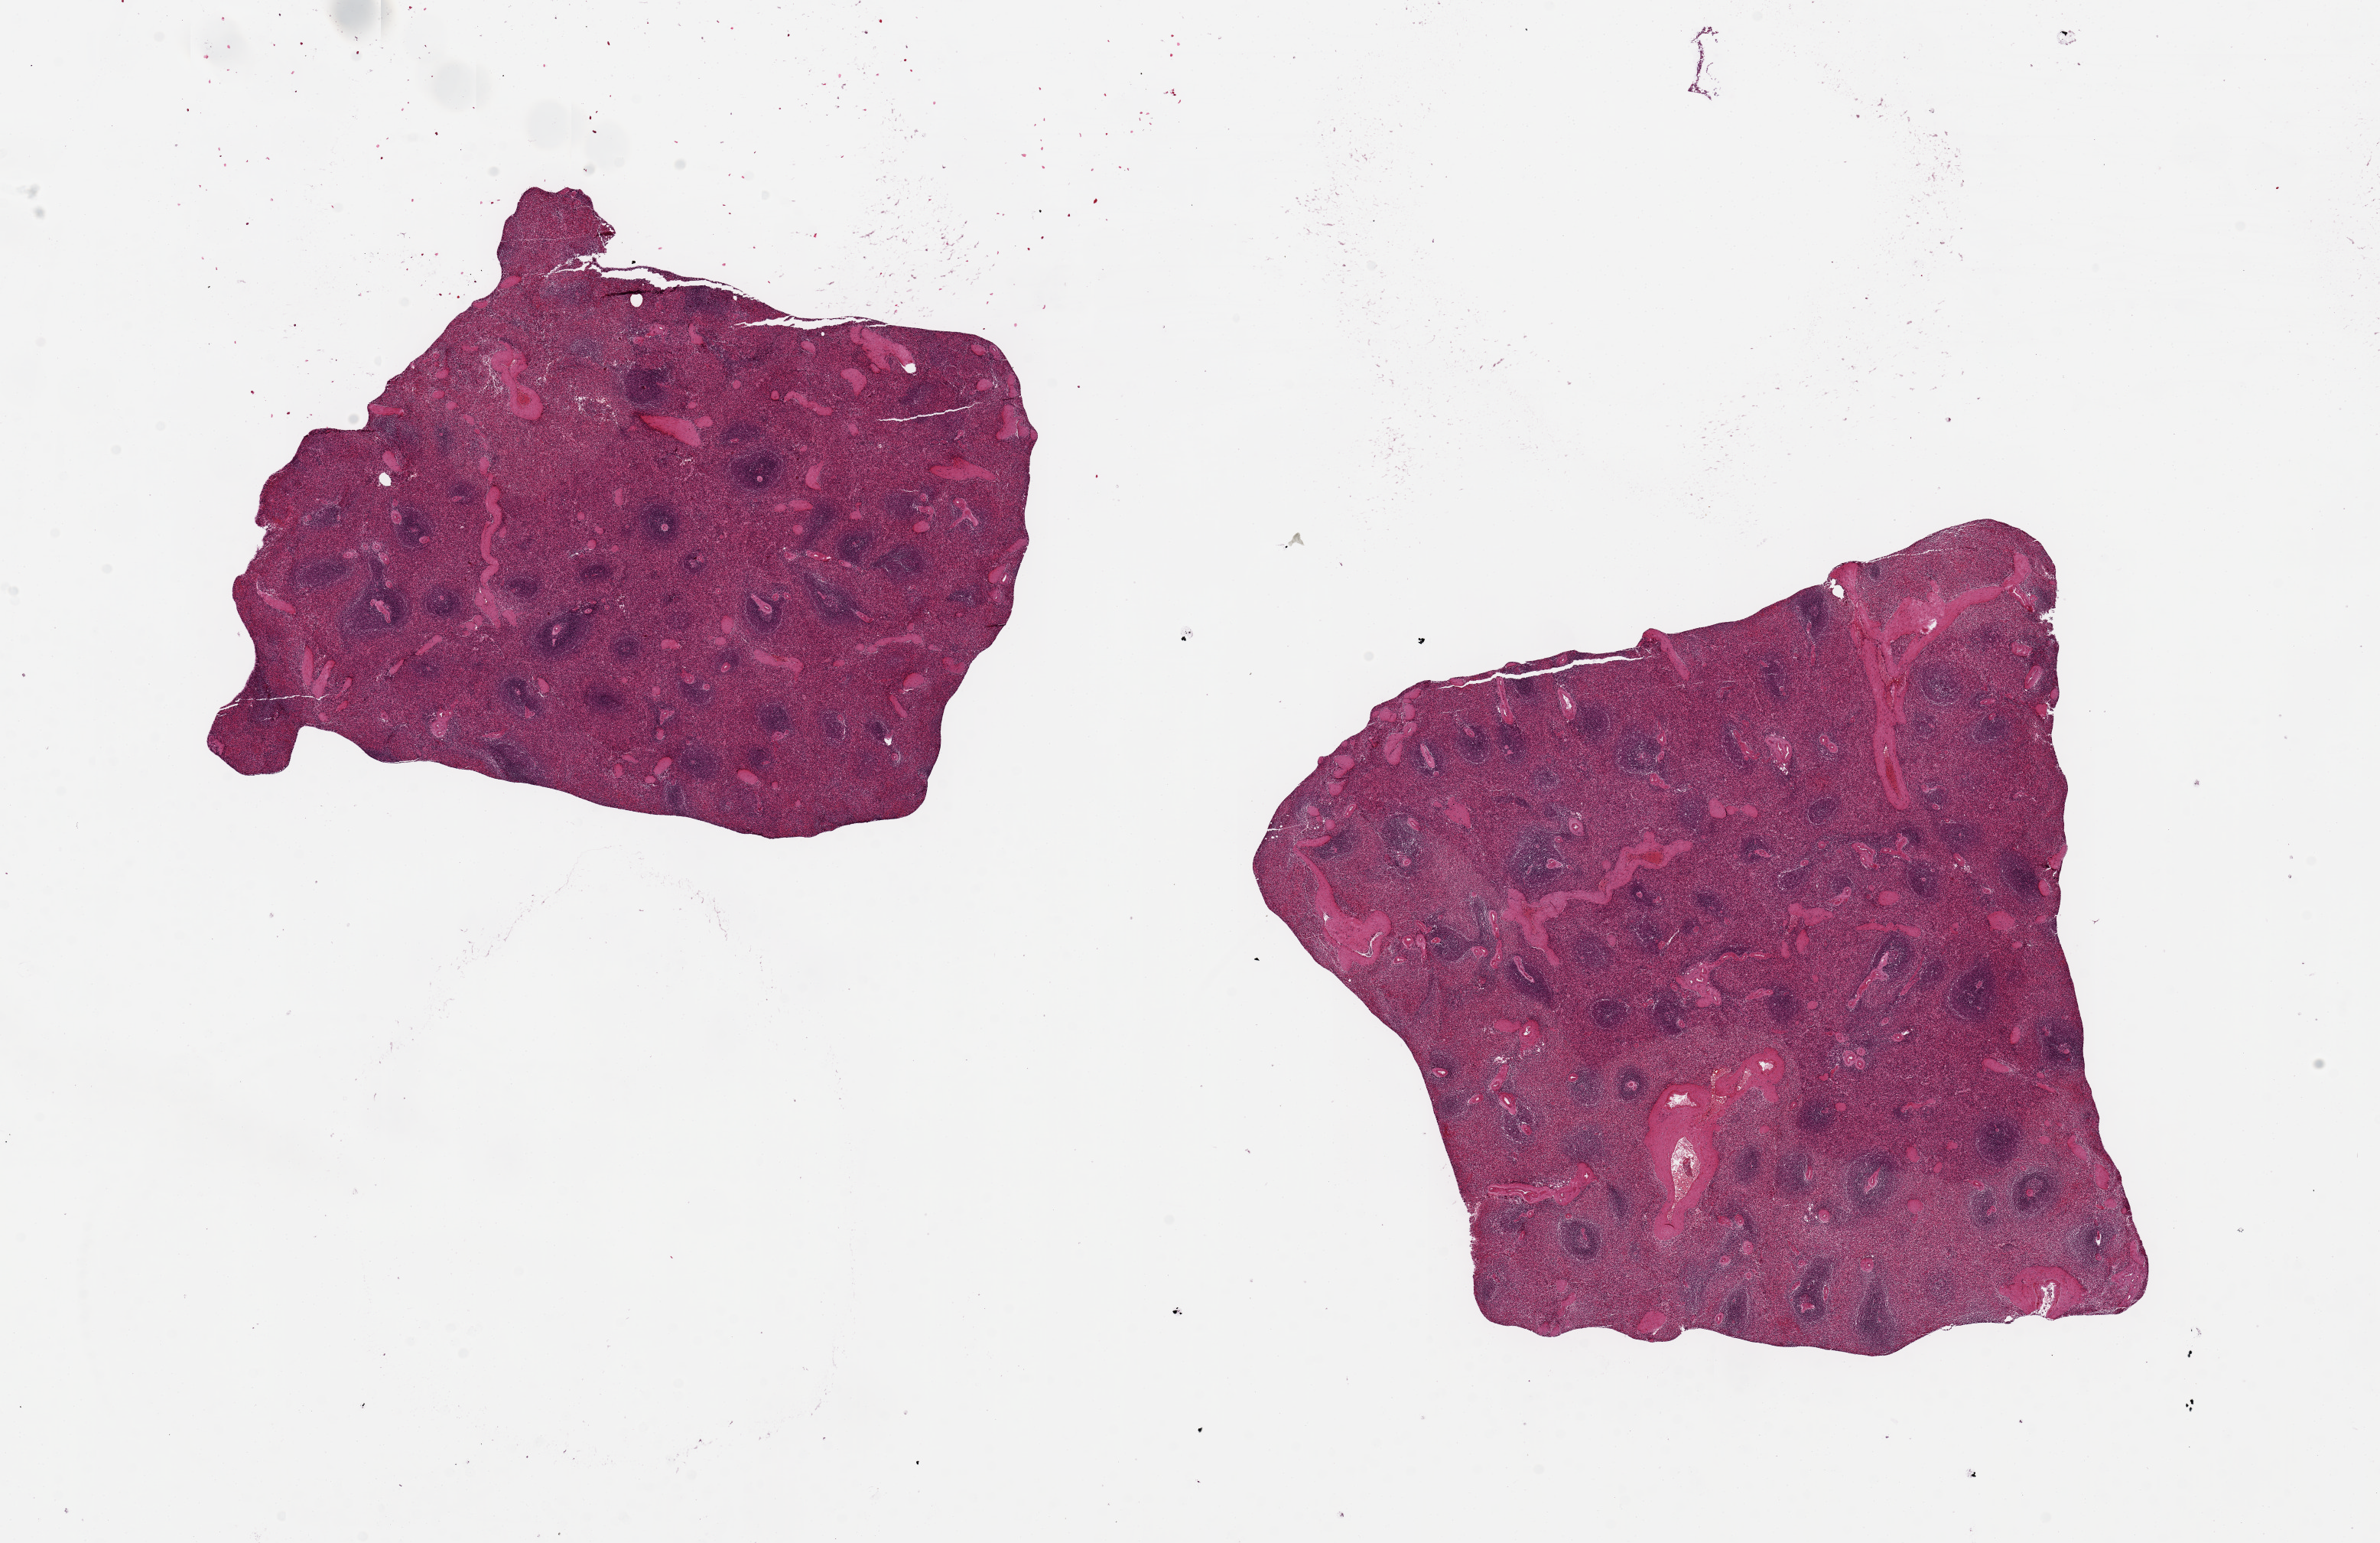
Whole-slide image, H&E stain, a low-resolution overview of the entire scanned area, about 24.6 x 16.0 mm (from a 20x scan); PAXgene-fixed paraffin-embedded (PFPE) section; section of spleen (target tissue); donor tissue sample. Donor sex: female.
Reviewer comment on this tissue sample: 2 pieces, 8x7 & 9x8mm; mild congestion.